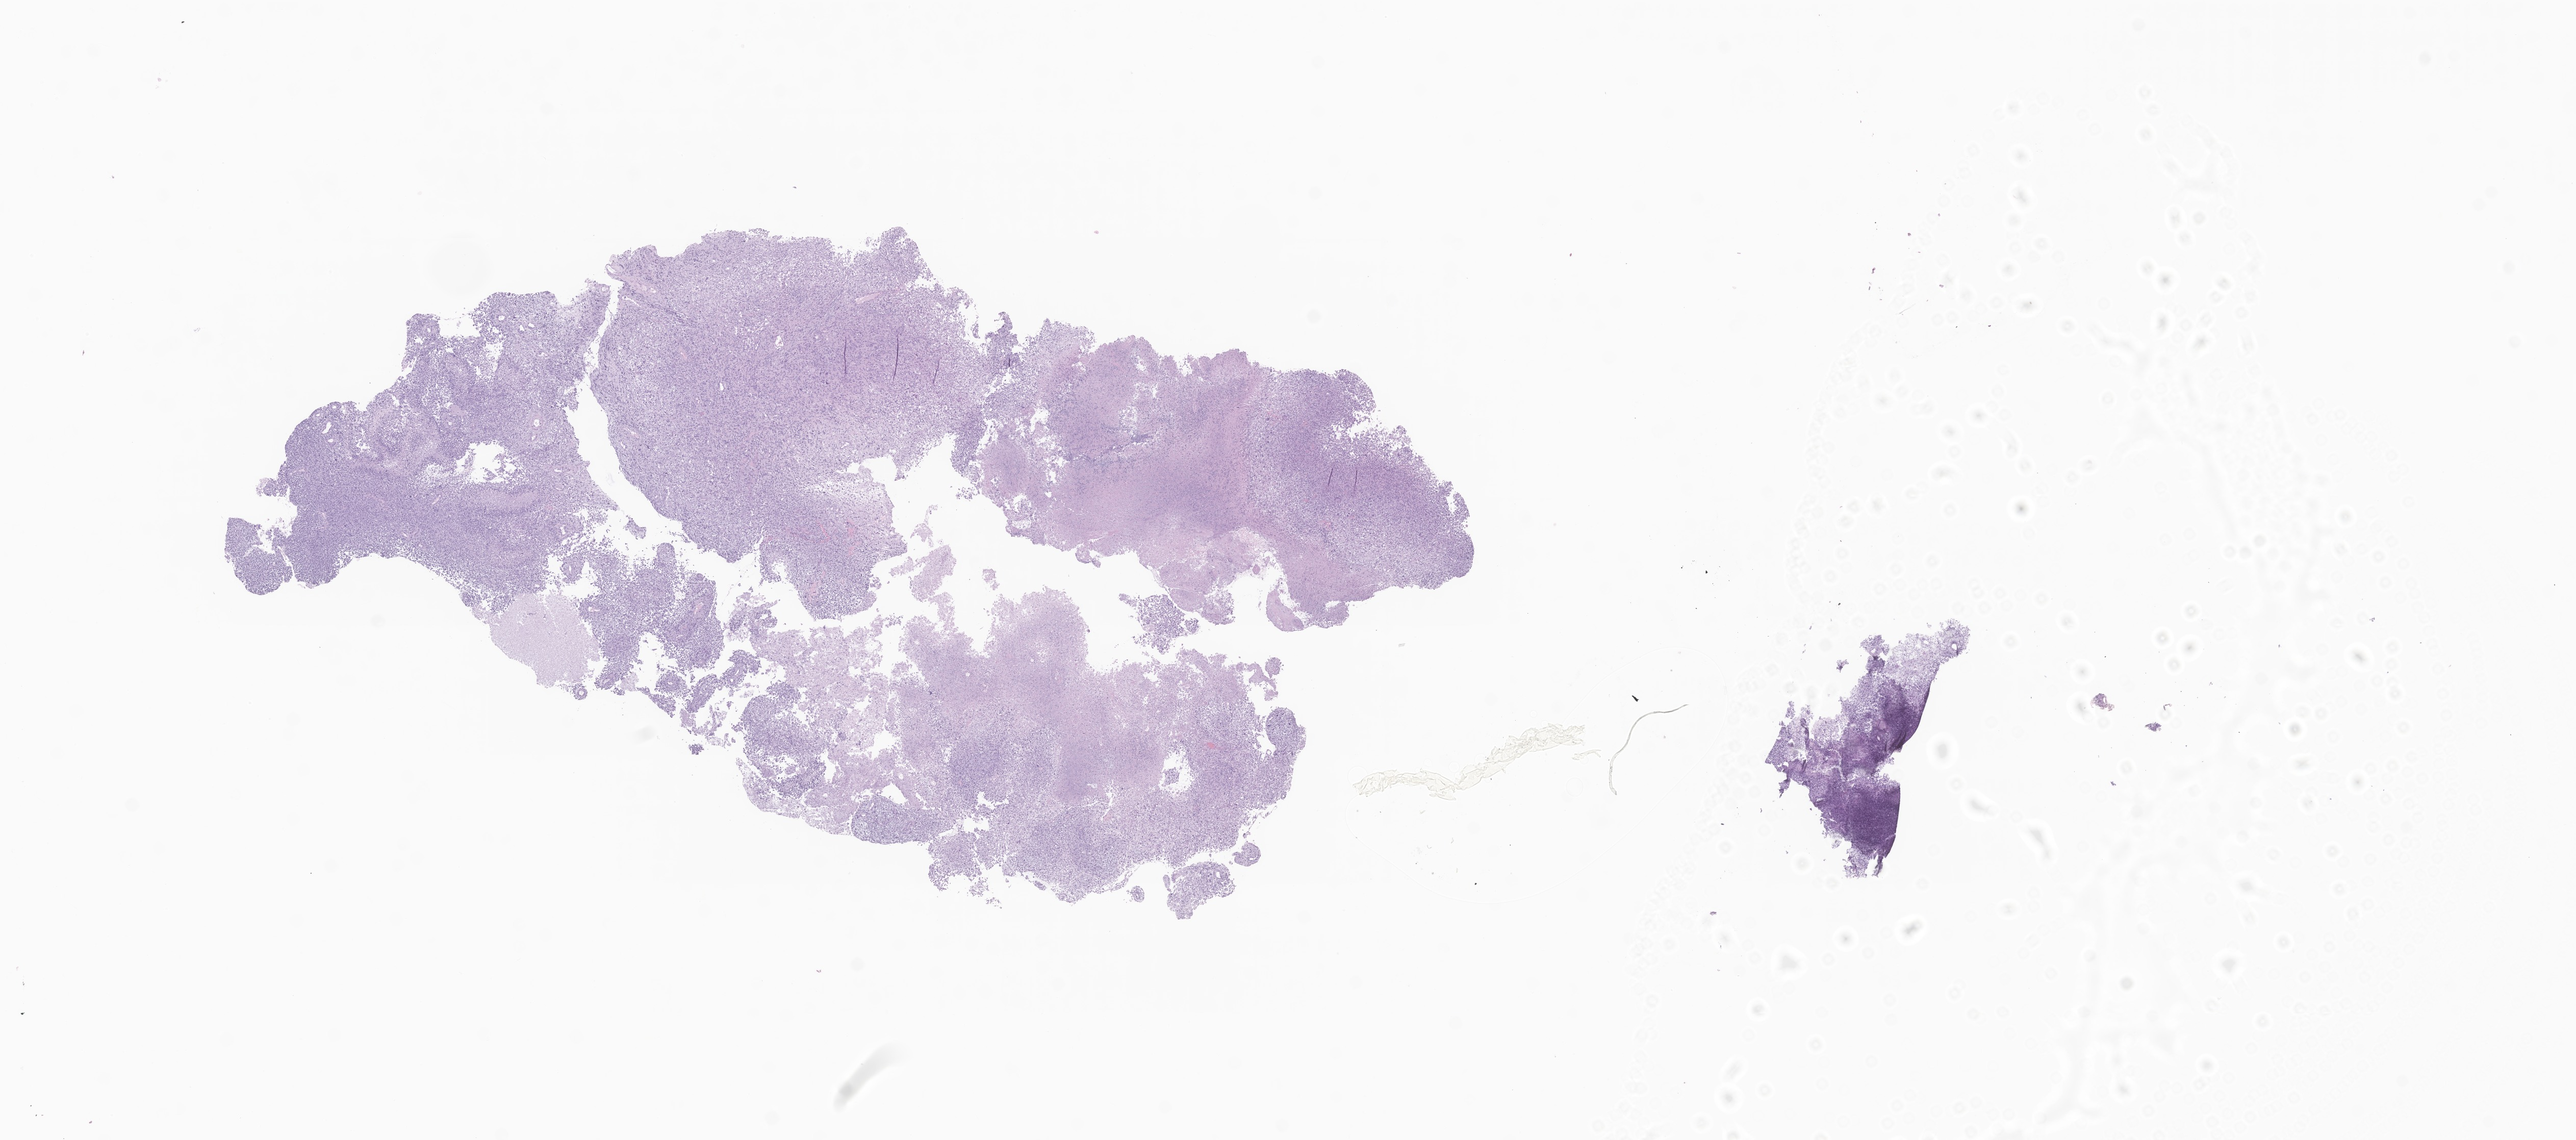
Haematoxylin and eosin whole-slide image of tumor tissue from the brain — whole scanned area (about 21.3 x 9.4 mm) shown as a low-resolution overview. Formalin-fixed paraffin-embedded section. Female patient, age 222 months (18 years 6 months).
Recorded diagnosis: Glioblastoma, NOS.